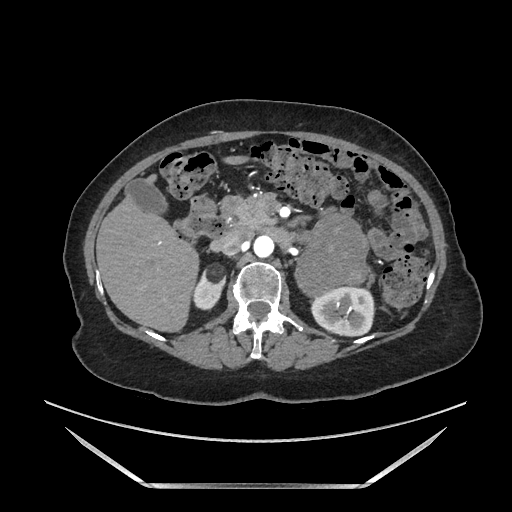
Contrast-enhanced abdominal CT, one axial slice. Slice 94 of 205 in the series (ordered by position). Soft-tissue window (W 400 / L 40 HU). 1.25 mm slice thickness. 512 × 512 image matrix, field of view 440 × 440 mm. Female patient. From the clinical record (not read from this slice): diagnosis: adrenocortical carcinoma; tumour side: left adrenal; tumour size at pathology: 12.5 cm; Ki-67 index: 39 %; stage (as recorded): 3.
Annotated regions visible in this slice (semi-automatic segmentation, software-assisted and operator-edited):
- mass: bounding box [x1, y1, x2, y2] px = [295, 219, 368, 294]